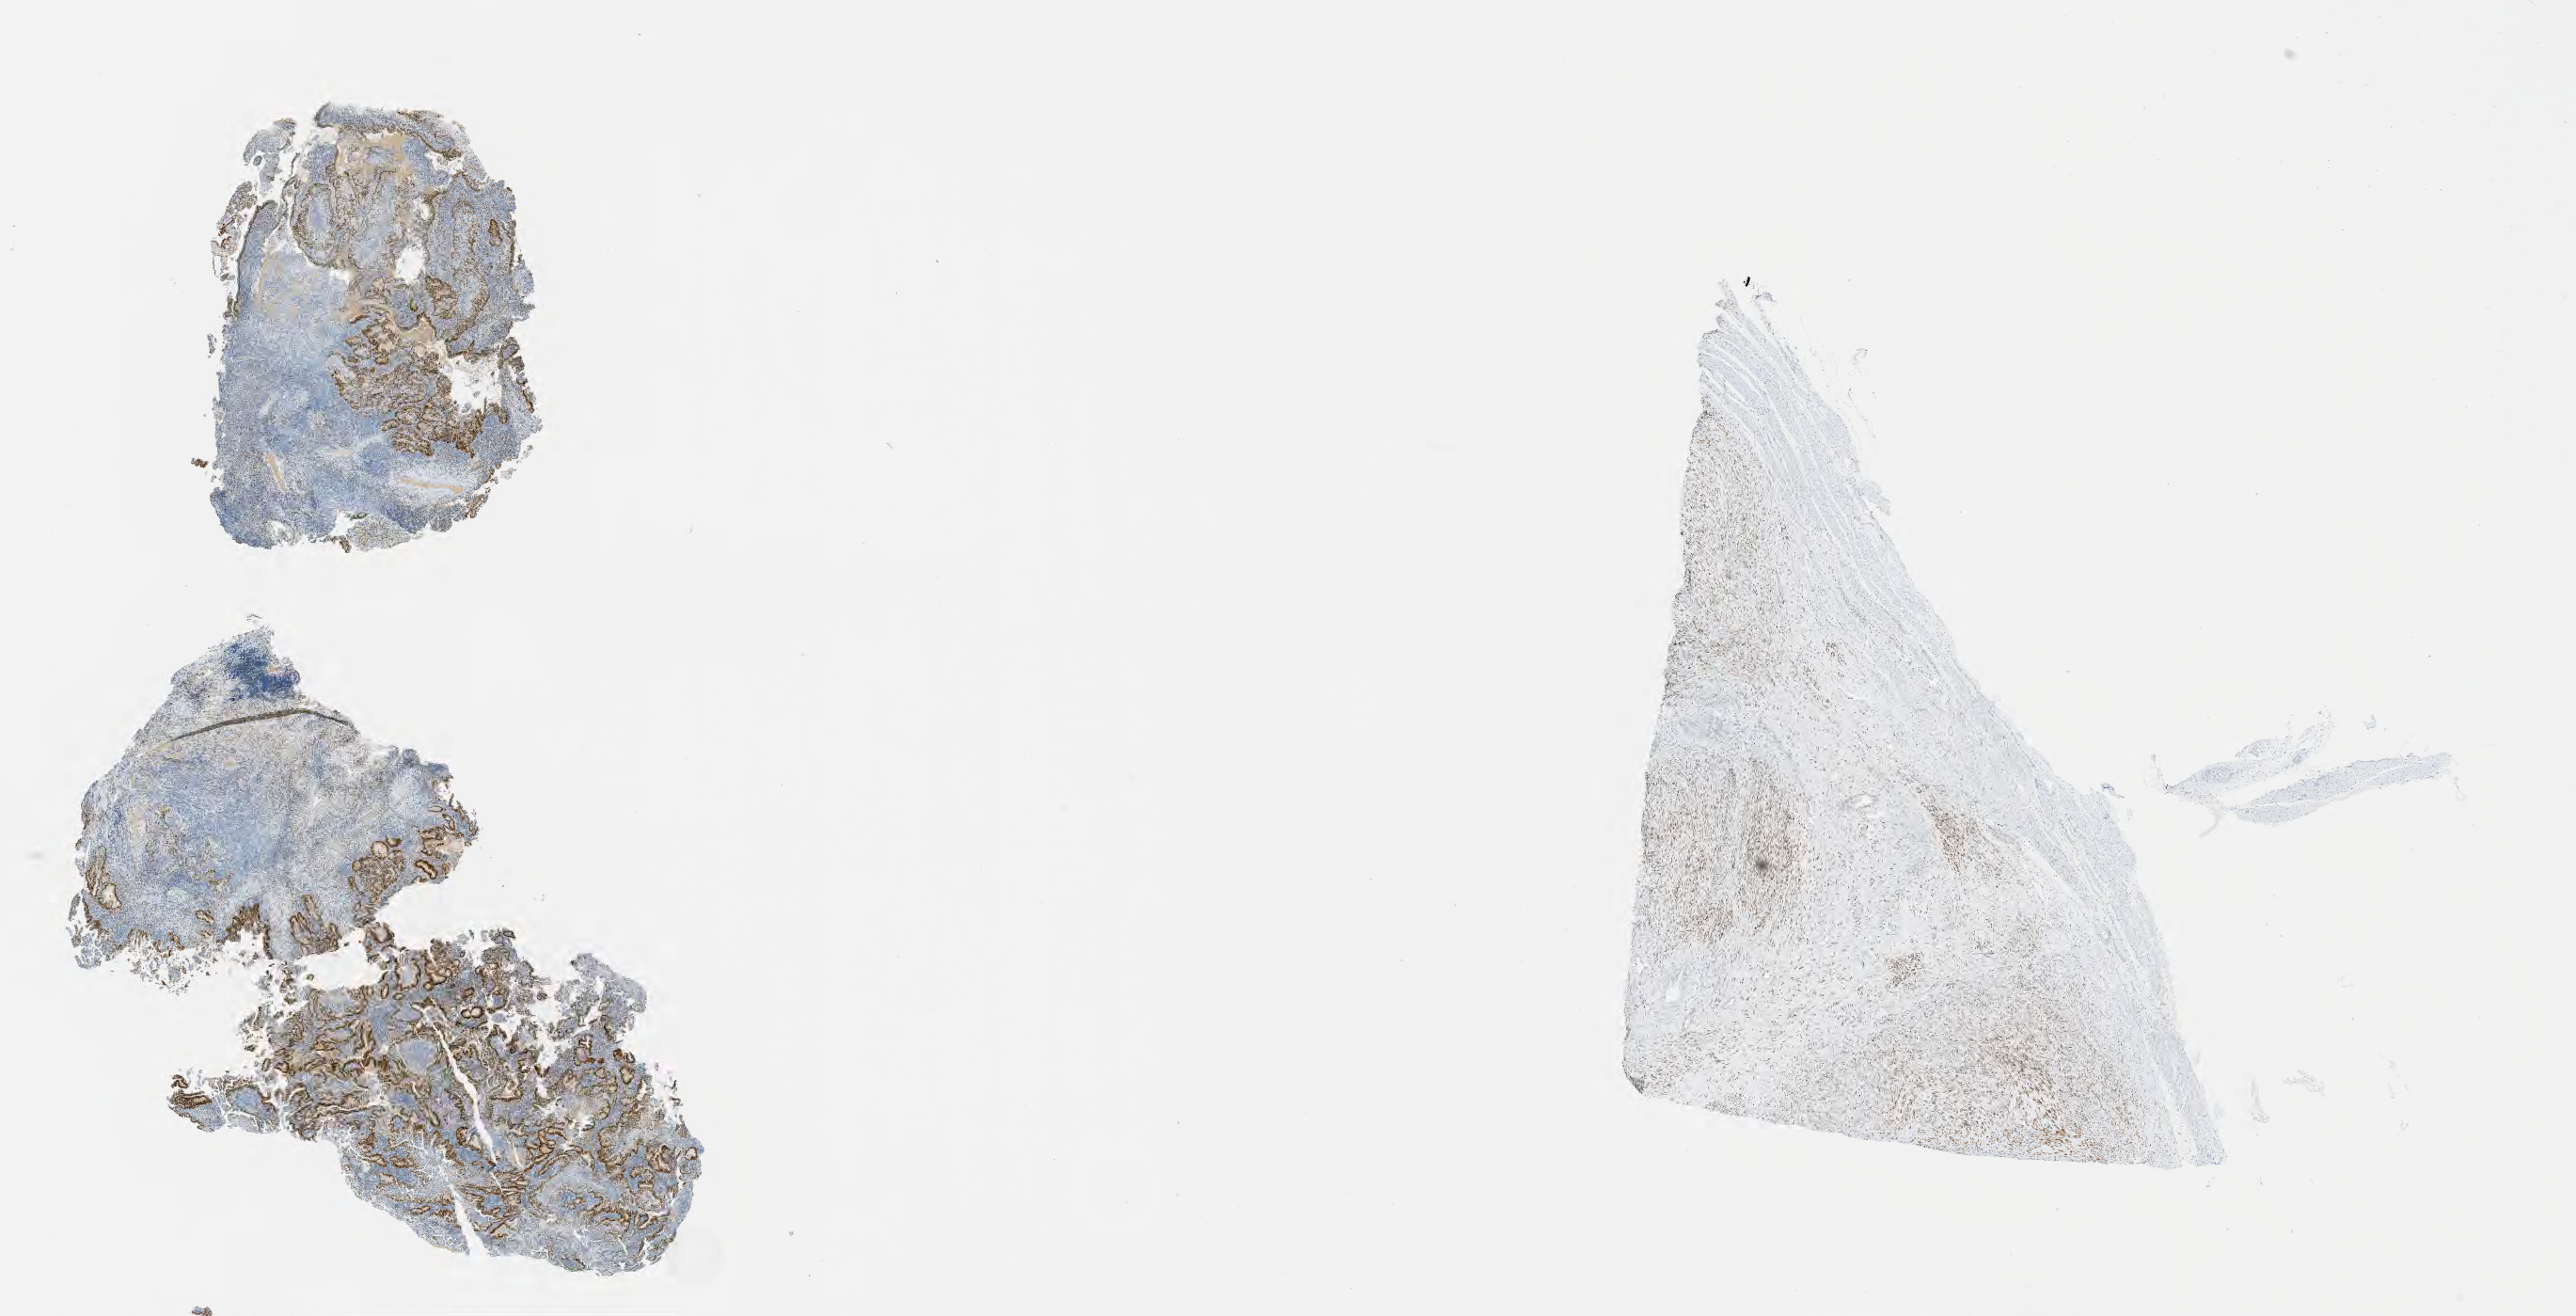
Immunohistochemistry (IHC) whole-slide image stained for estrogen receptor (ER) — a low-resolution overview of the entire scanned area, about 22.1 x 11.3 mm; tumor tissue; site: cervix. Female patient, age 48 years.
Histologic diagnosis: Adenocarcinoma, NOS.